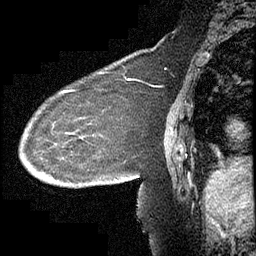
Breast MRI (dynamic contrast-enhanced), one sagittal slice. Slice 147 of 232 in the series (ordered by position). Dynamic contrast-enhanced study with each time point stored as its own series, time point 2 of 4 at this slice position (early post-contrast, ordered by acquisition time). 1.5 T. TE 4.2 ms, TR 6.7 ms. 256 × 256 image matrix, field of view 200 × 200 mm. Female patient, age 63 years. From the clinical record (not read from this slice): setting: breast cancer imaged before/during neoadjuvant chemotherapy; receptor status: triple-negative.
Annotated regions visible in this slice (semi-automatic segmentation, software-assisted and operator-edited):
- analysis volume of interest (the breast-tissue region the enhancement analysis was run in; not a lesion): bounding box (x1, y1, x2, y2) in pixels: (19, 90, 140, 211)
- tumour enhancement mask (voxels above the 70 % enhancement threshold inside the analysis volume of interest): (60, 90, 116, 180)